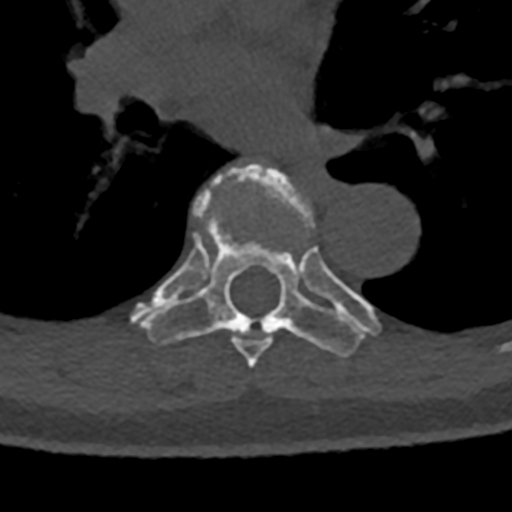
CT including the spine, one axial slice. Position 778 of 797 along the scan axis. 120 kVp. Bone window (W 1800 / L 400 HU). 0.5 mm slice thickness. 512 × 512 image matrix. Male patient, age 74 years. Case-level facts recorded for this patient, not image findings: primary cancer: renal; vertebrae with lytic lesions (as recorded): T10, L1, L2, L3, L4, L5.
Structures marked on this image (semi-automatically segmented with operator editing):
- T6 vertebra: bounding box (x1, y1, x2, y2) in pixels: (176, 166, 312, 368)
- T7 vertebra: (132, 205, 378, 357)